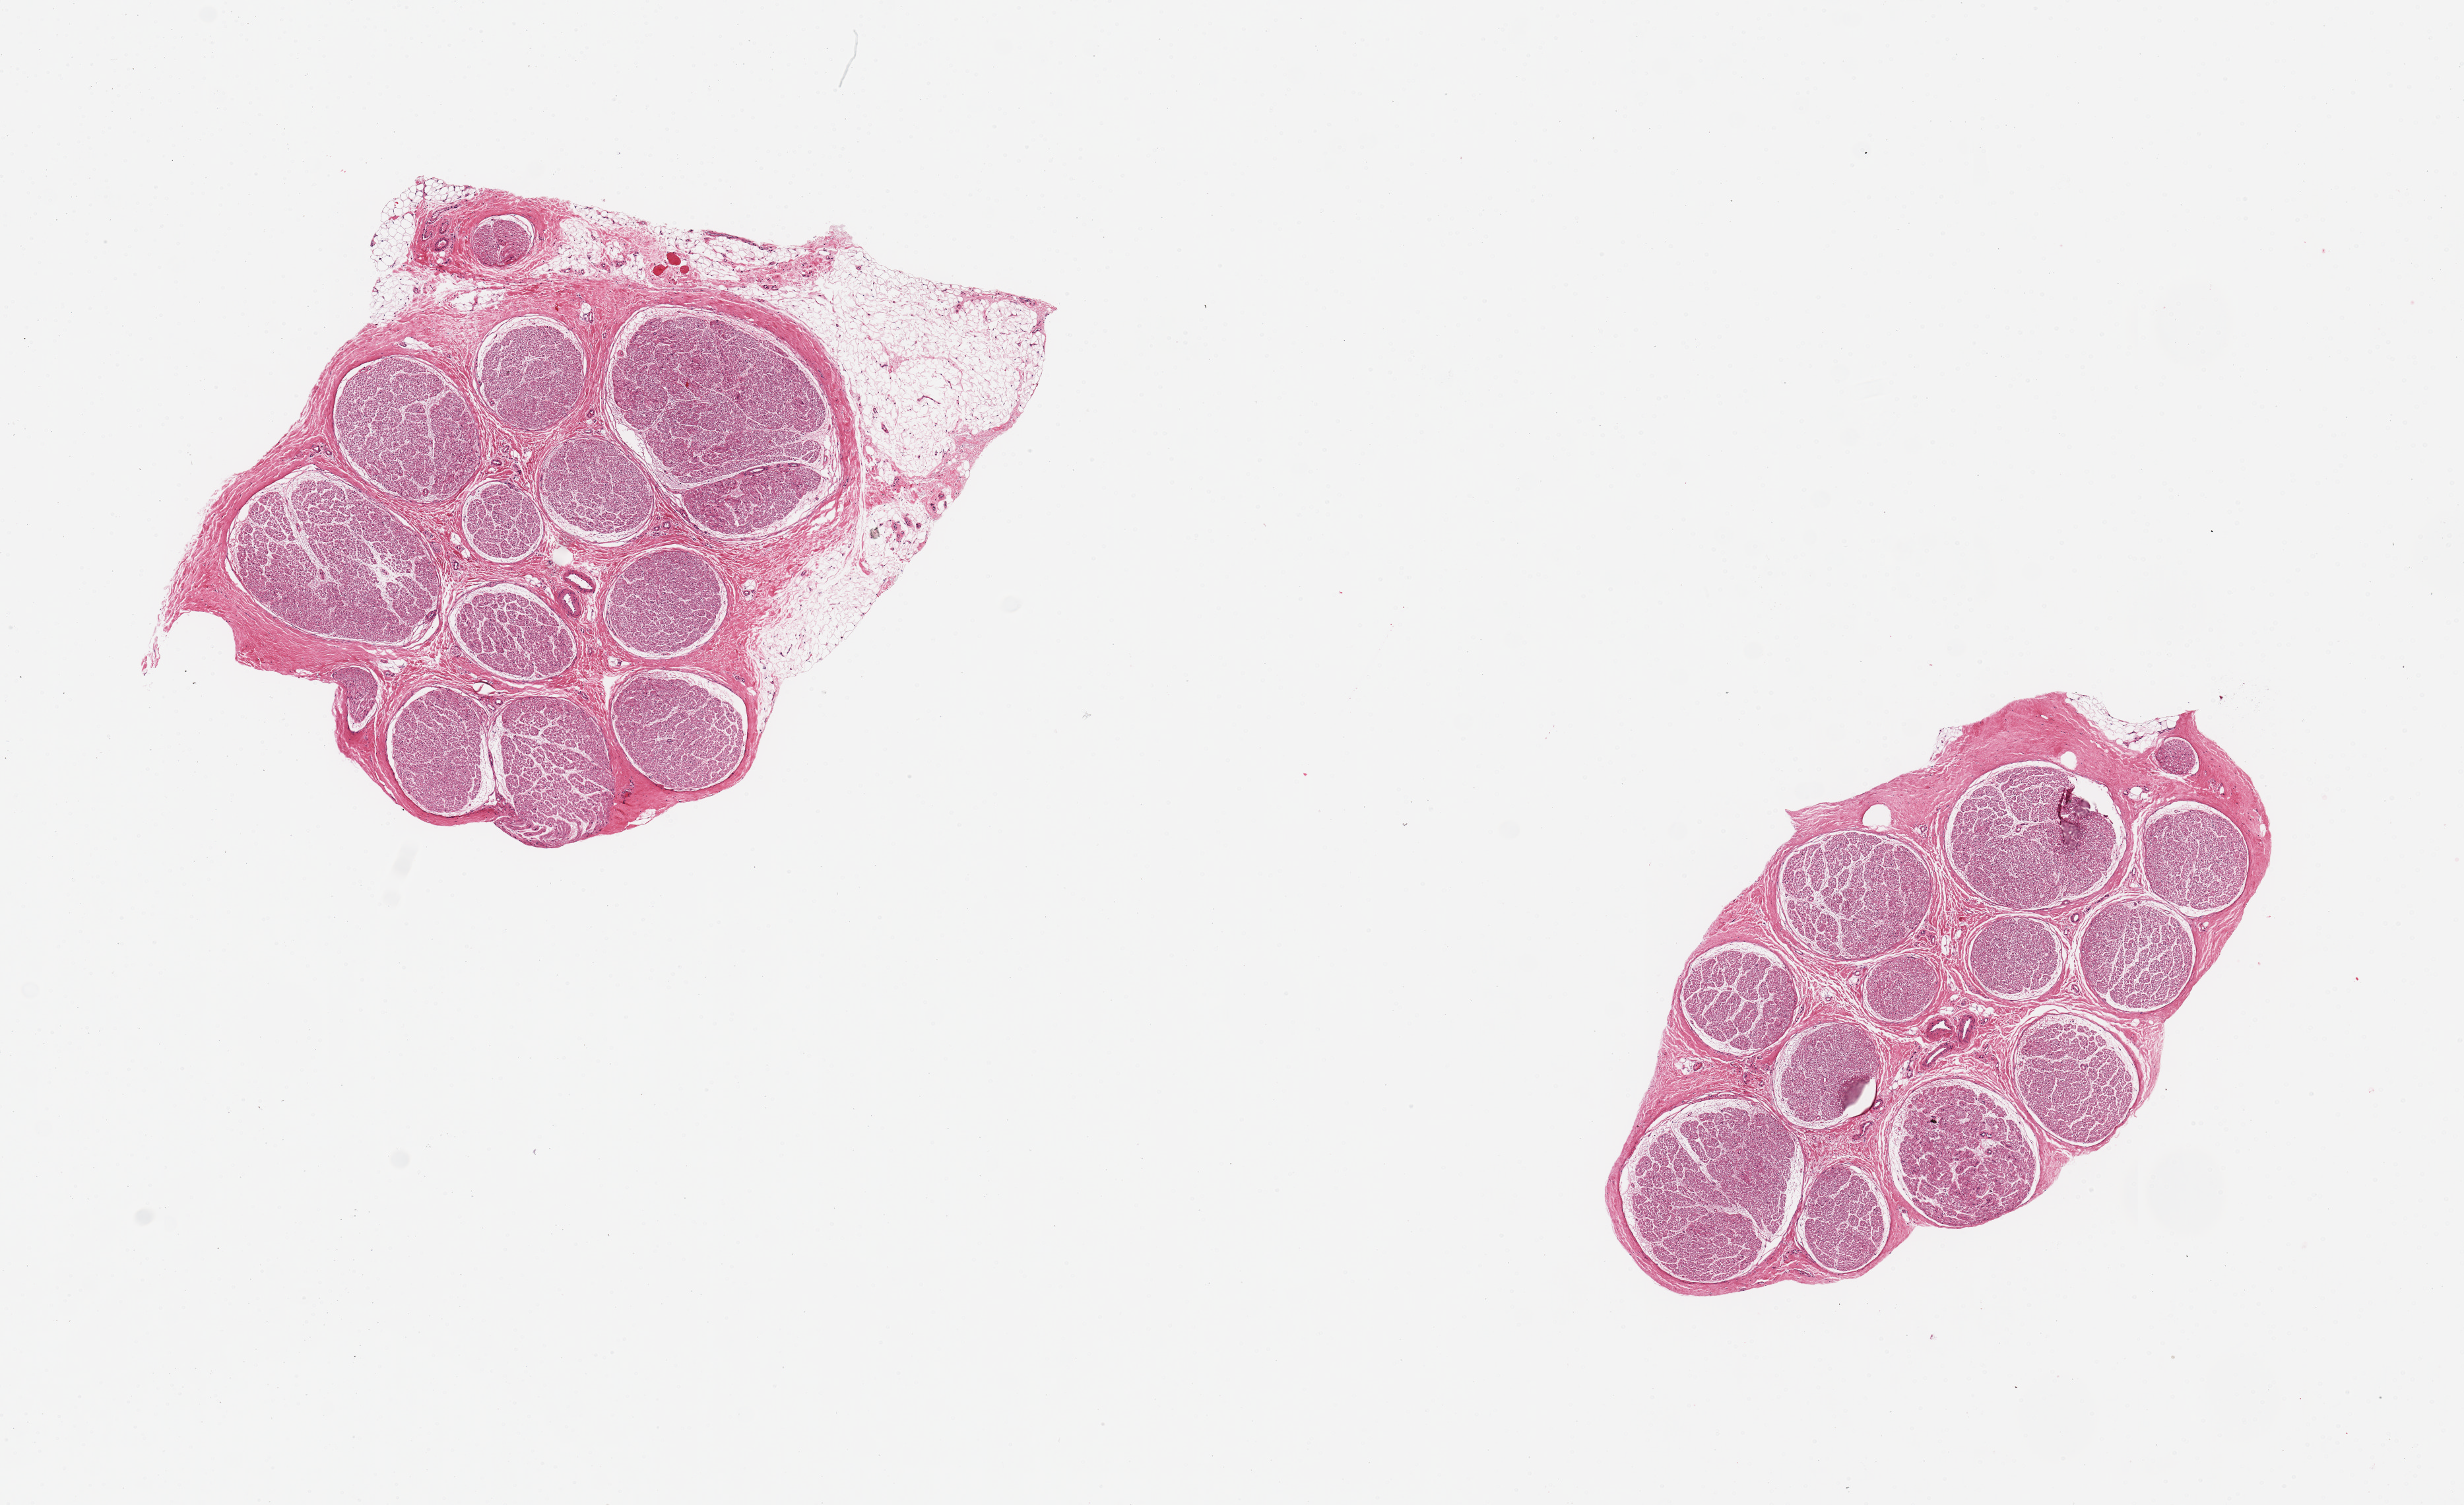
Digitized haematoxylin and eosin-stained section, a low-resolution overview of the entire scanned area, about 14.8 x 9.0 mm (from a 20x scan). PAXgene-fixed, paraffin-embedded tissue. Section of tibial nerve (target tissue). Donor tissue sample.
Reviewer comment on this tissue sample: 2 pieces, ~4.5x2.5; one with 20% fat on edge.